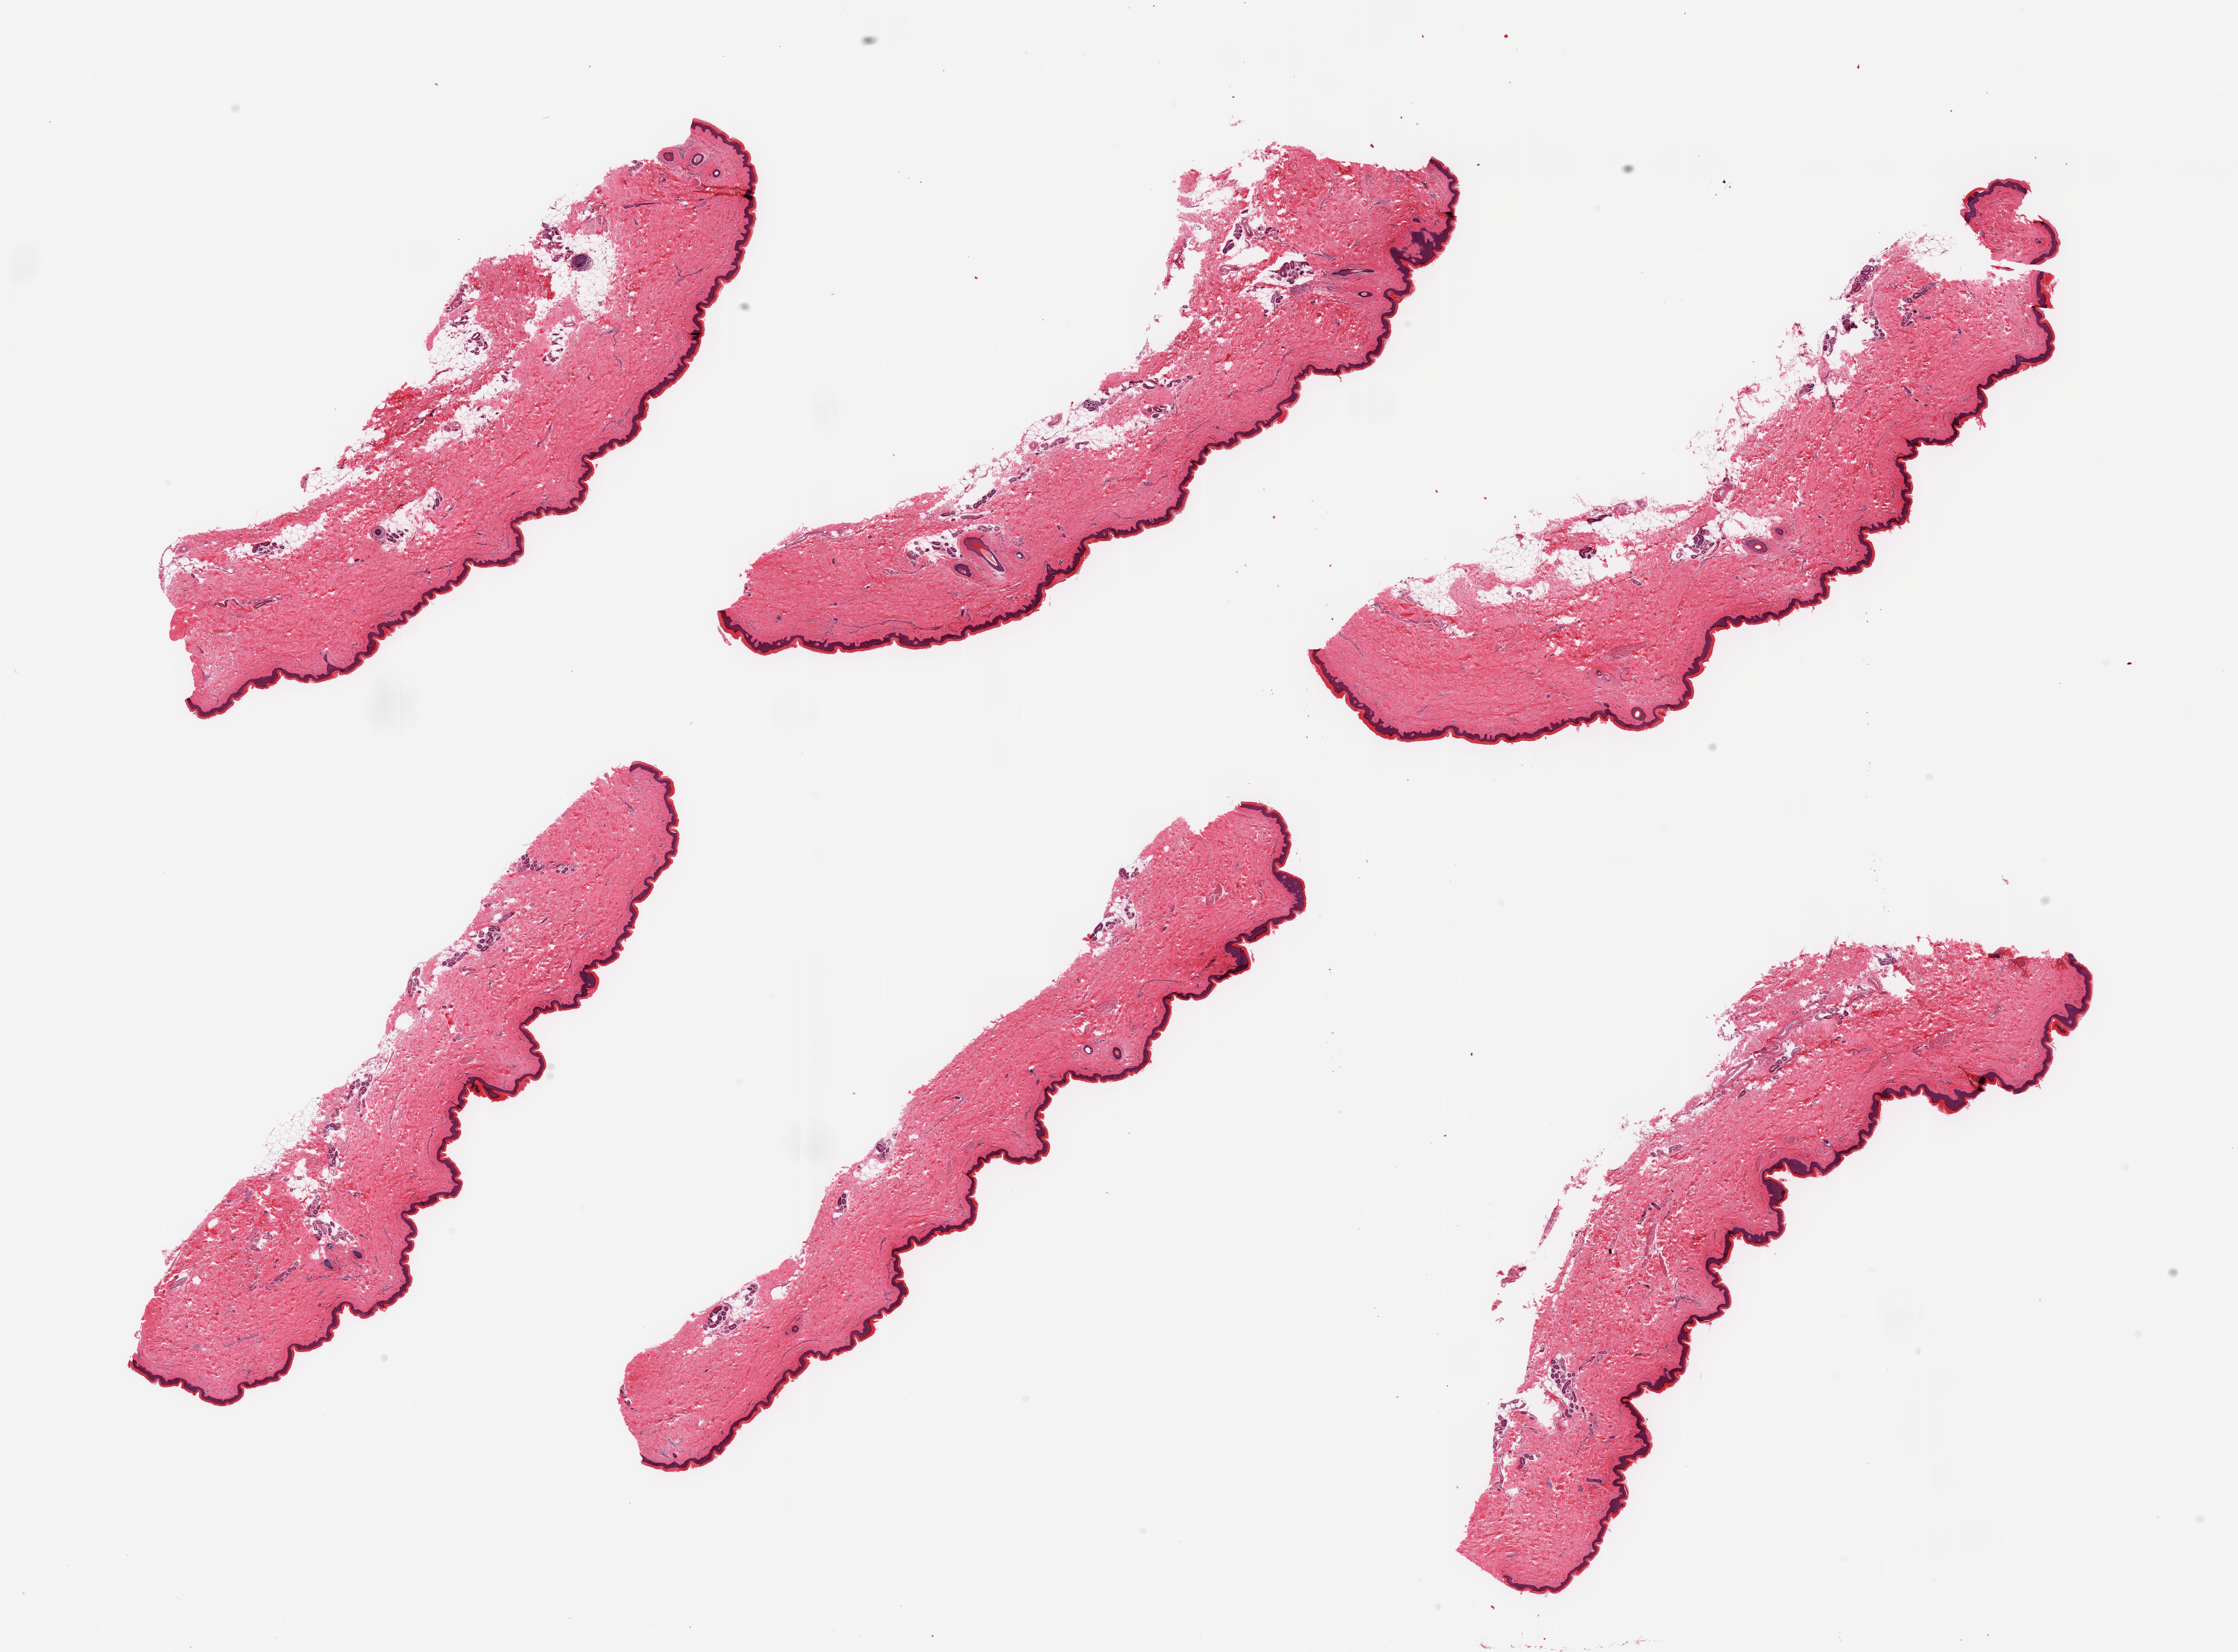
Haematoxylin and eosin whole-slide image — a low-resolution overview of the entire scanned area, about 27.6 x 20.4 mm (slide scanned at 20x). PAXgene-fixed, paraffin-embedded tissue. Target tissue: skin of lower leg. Tissue donor sample. Donor: female.
Review note (as recorded): 6 pieces; includes up to 10% internal/attached fat, epidermis measures 52 microns.